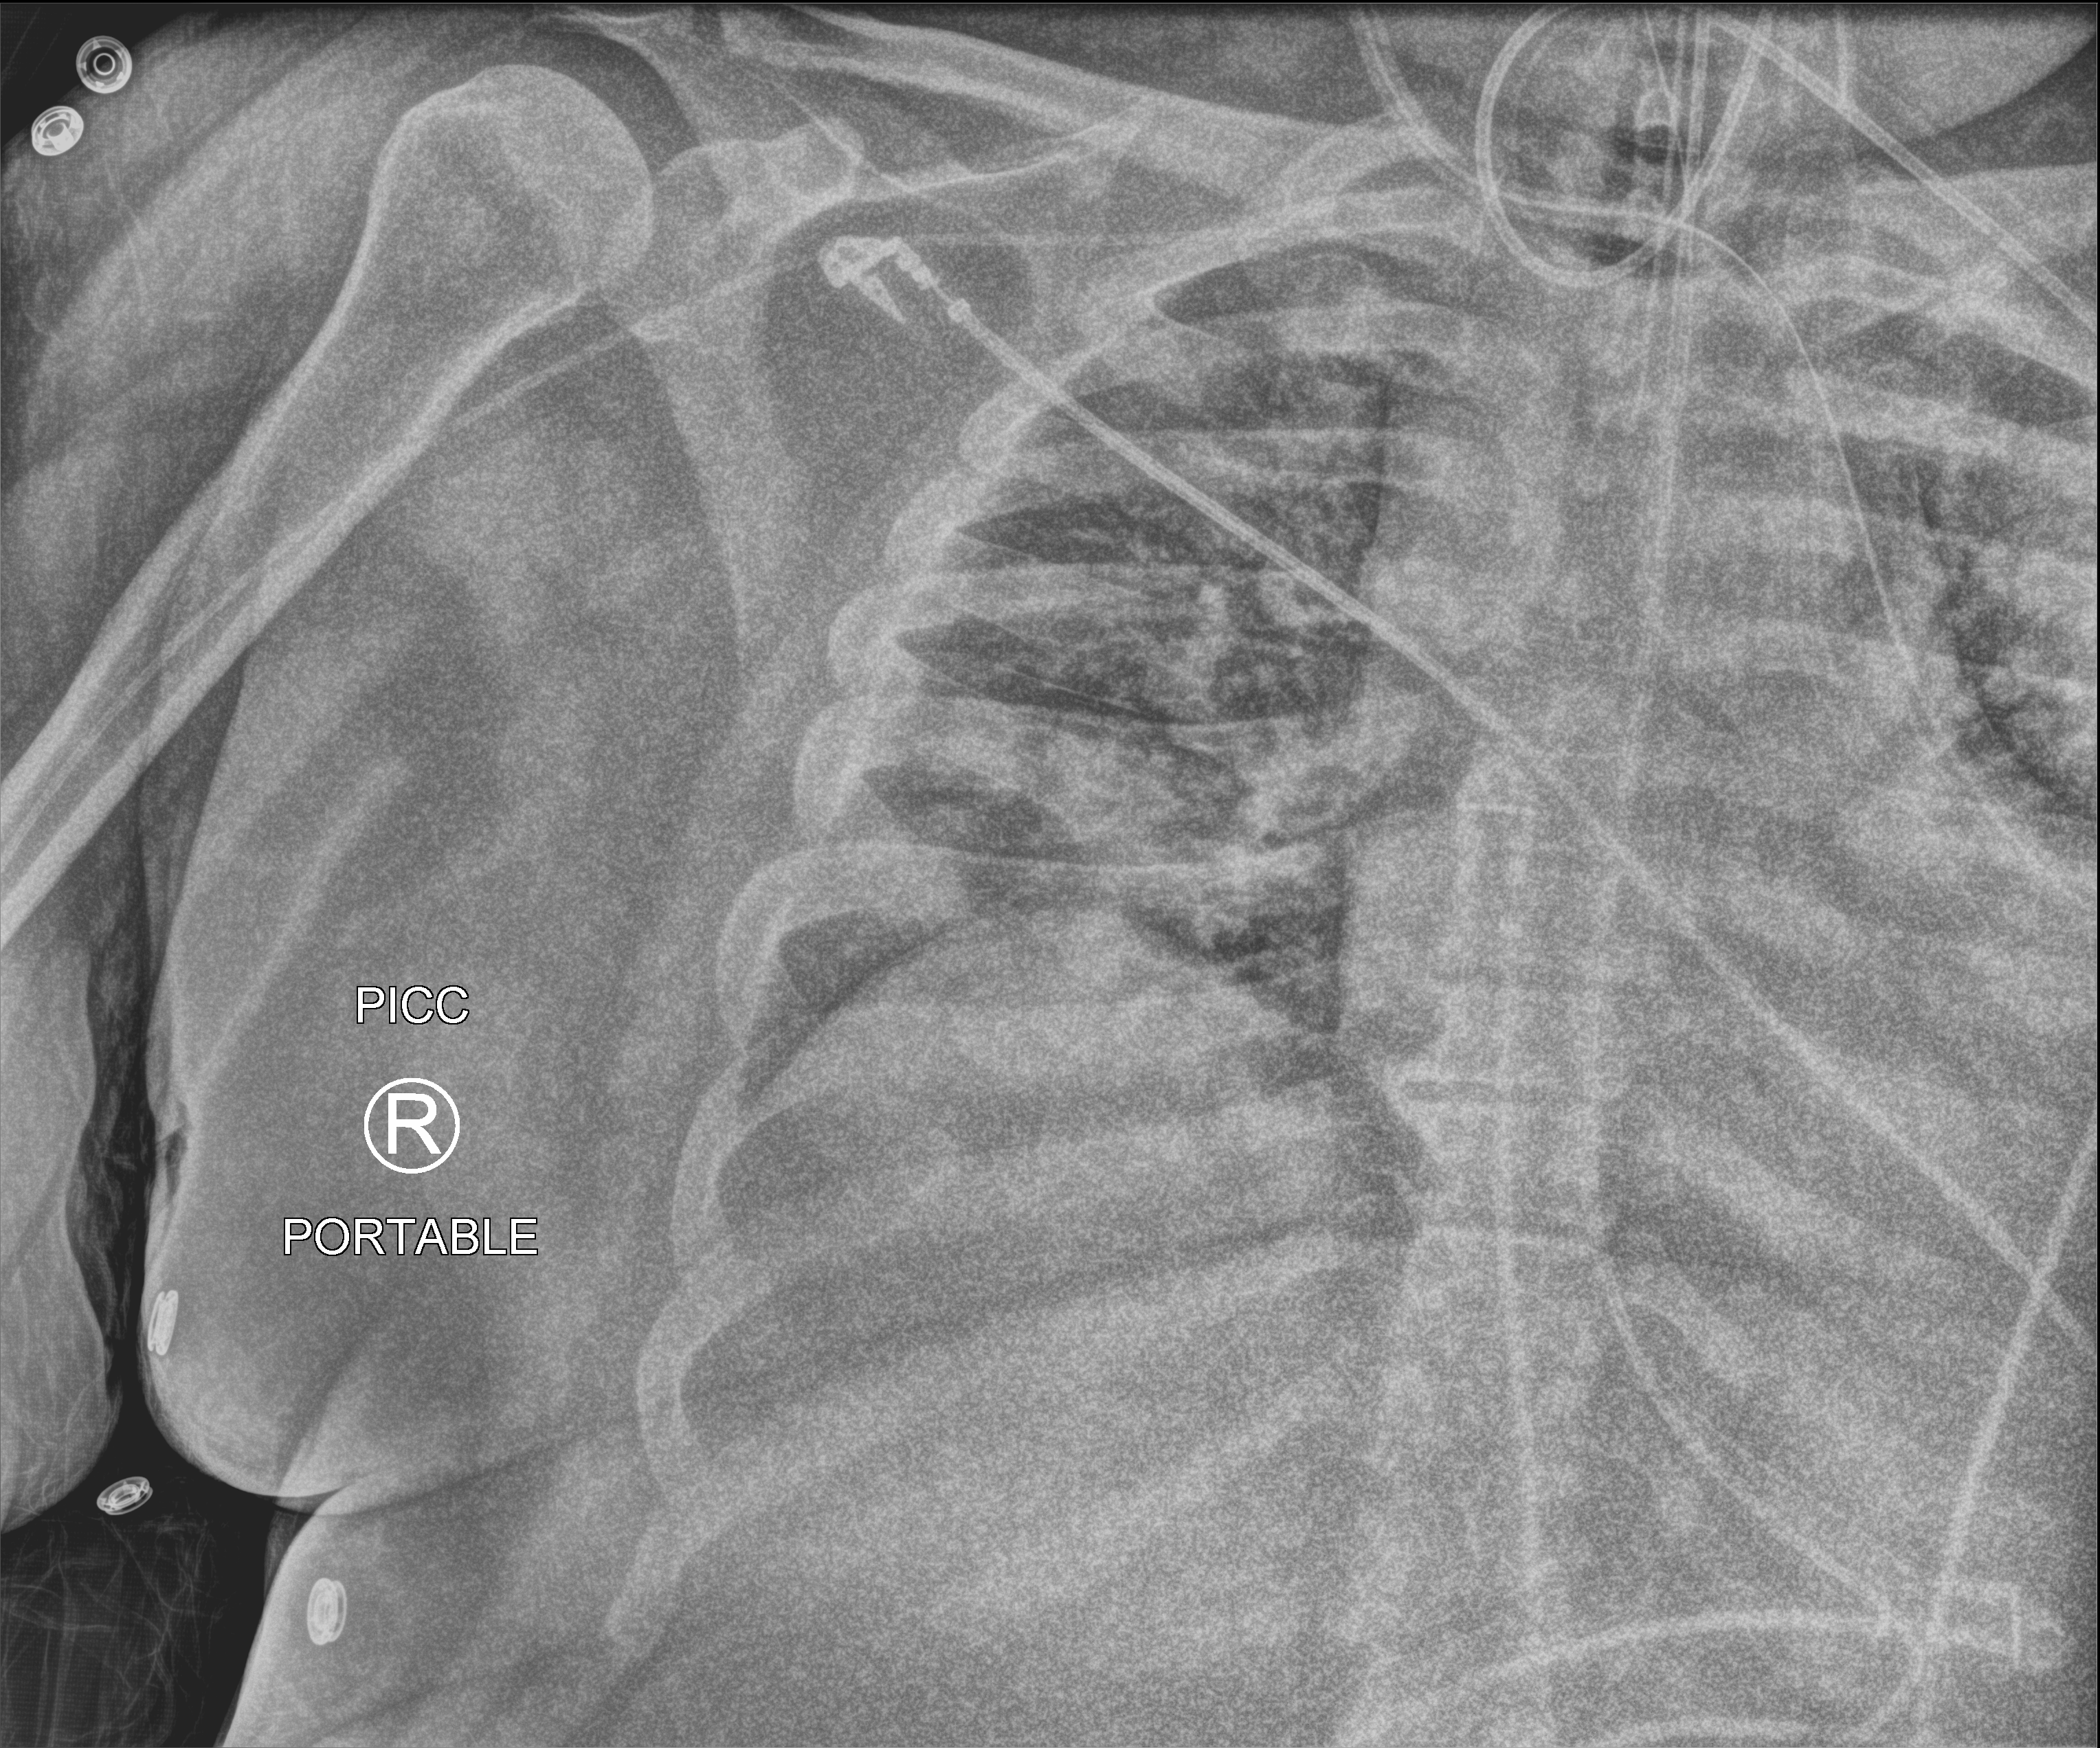
Chest X-ray (portable), anteroposterior (AP) projection. Patient hospitalised with COVID-19, aged 18–59 years.
From the hospital-stay record, not from the radiograph (when in the stay this image was taken is not recorded): mechanically ventilated during this hospital stay: yes; length of hospital stay: 10 days.